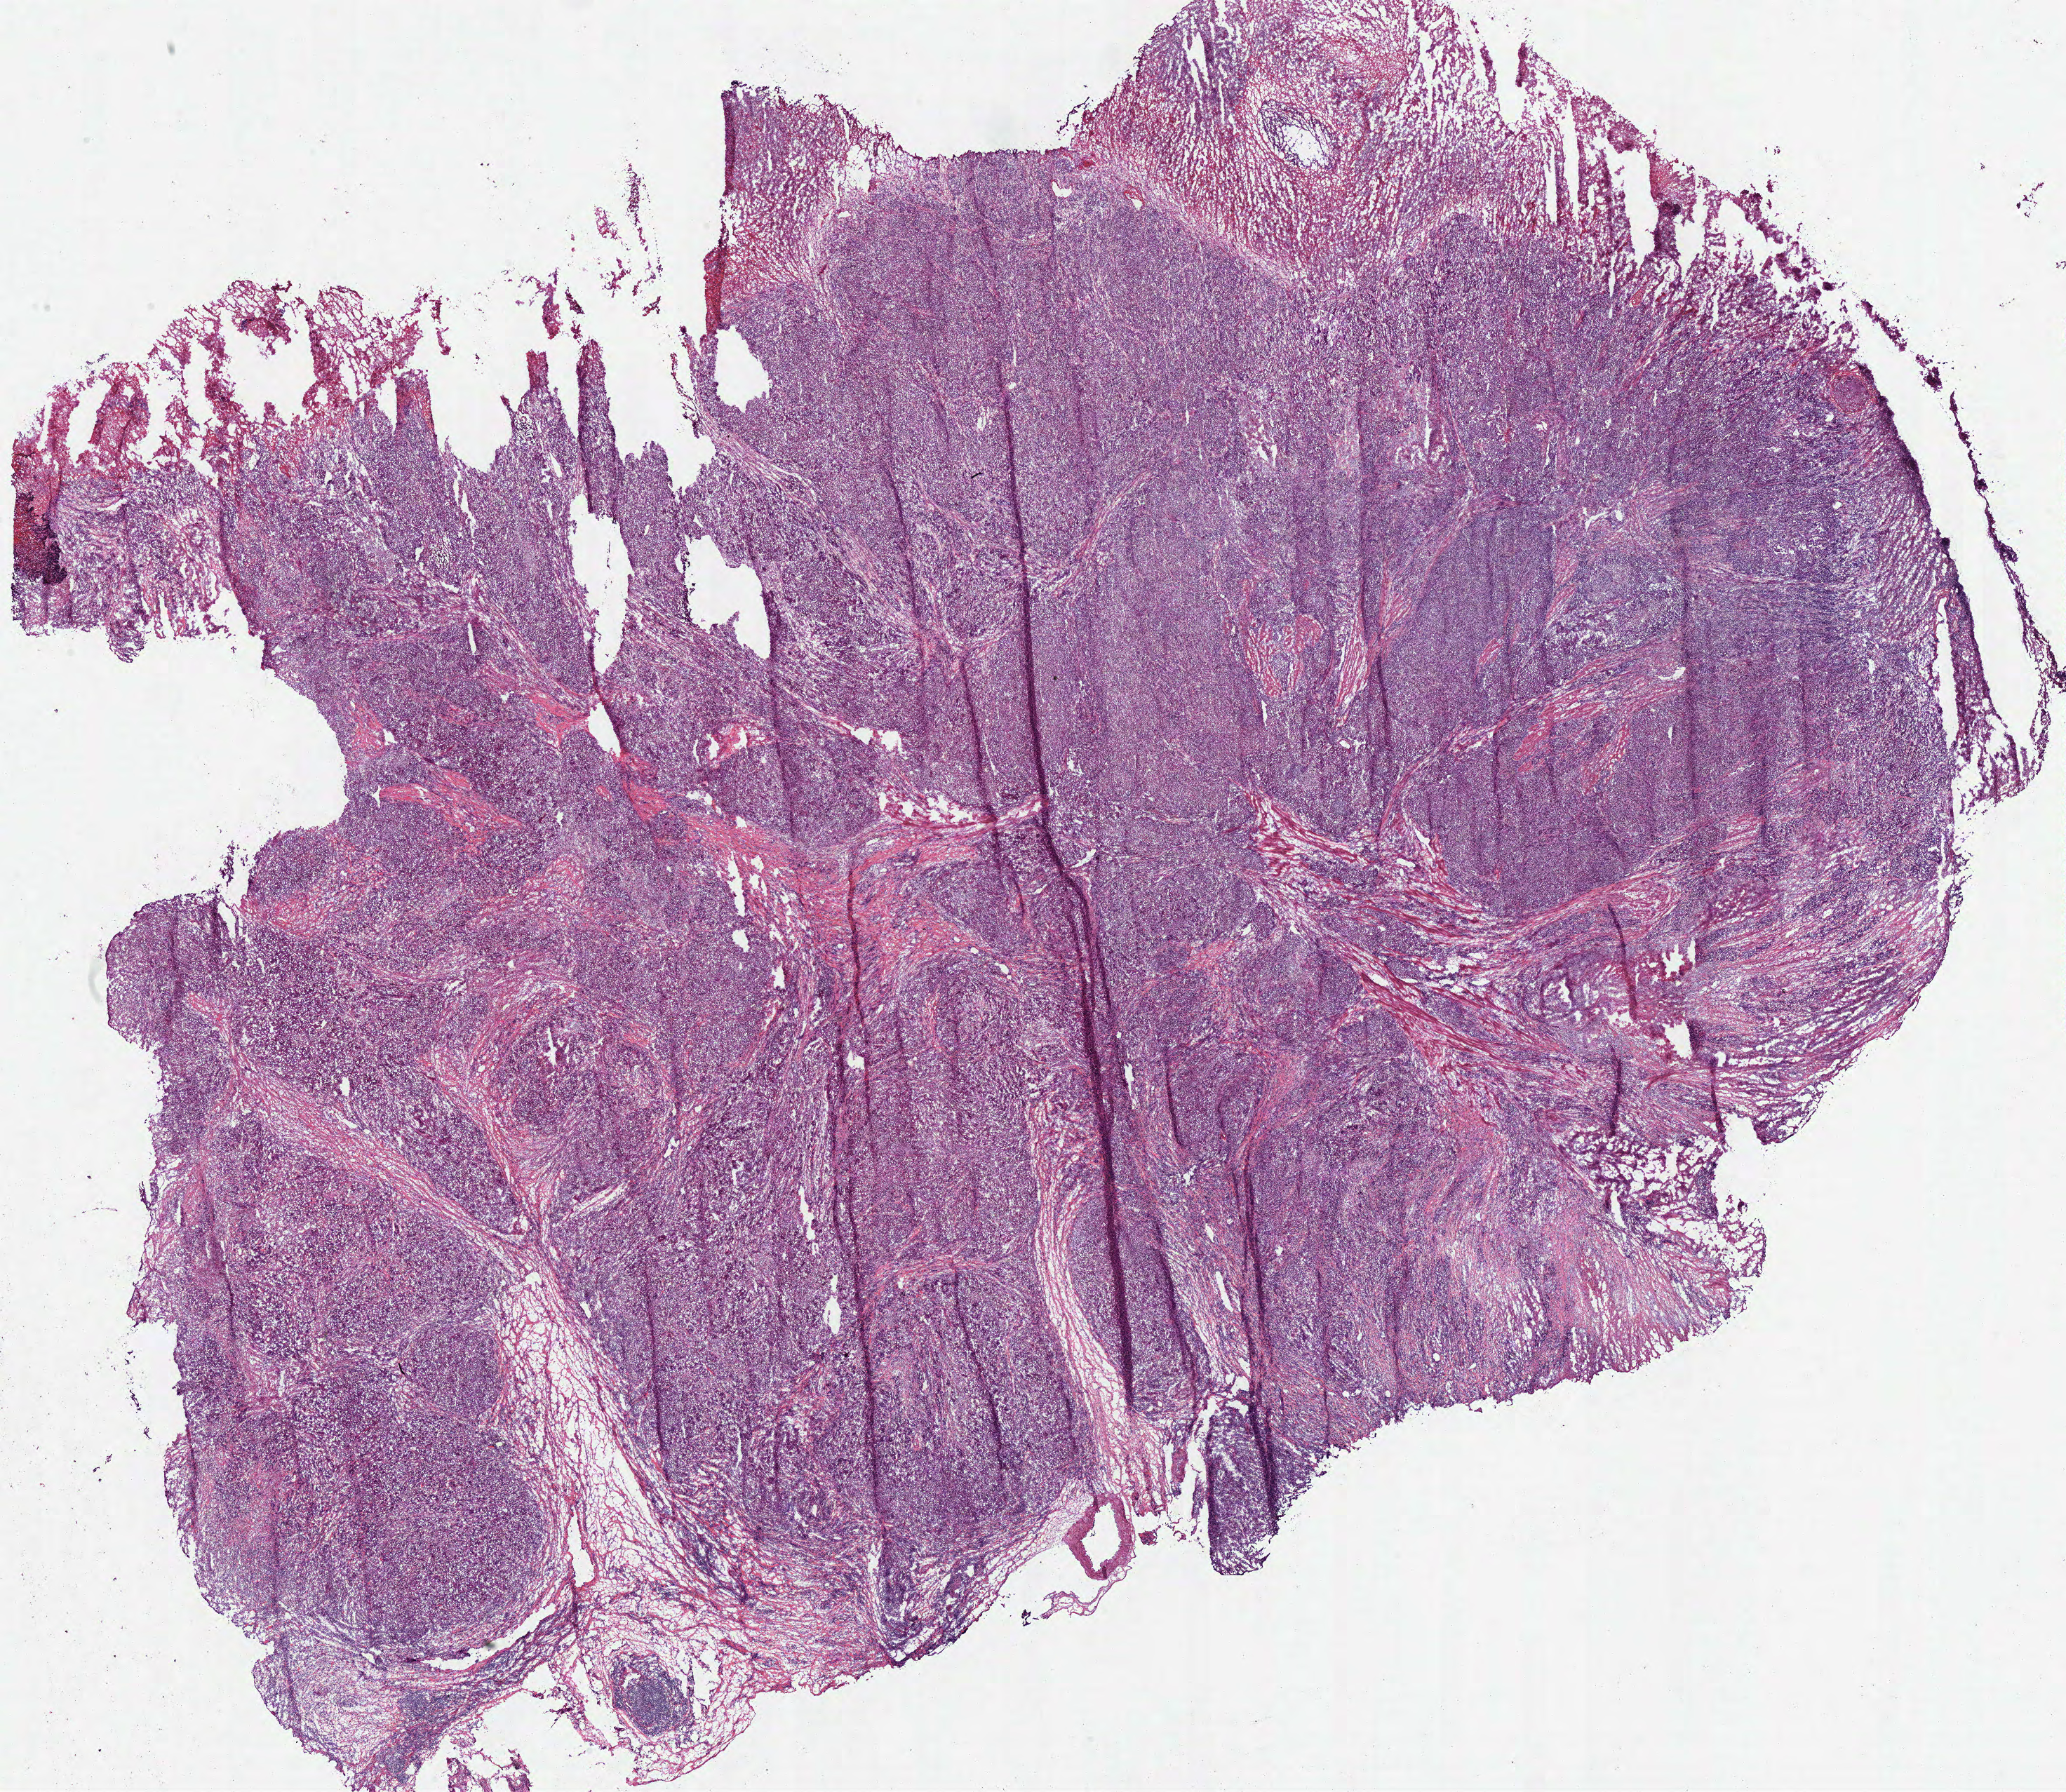
Digitized Hematoxylin and eosin (H&E) stained tissue section (whole slide) — whole scanned area (about 23.2 x 20.1 mm, acquisition: 40x scan) shown as a low-resolution overview, frozen section from the top of the tissue portion, sample: primary tumour, stomach. Female patient; age at initial diagnosis 64 years. Histologic grade: G3 (poorly differentiated). Slide review estimates, as recorded: tumour cells 95%, tumour nuclei 90%, normal cells 0%, stromal cells 5%, necrosis 0%.
Pathologic diagnosis: Adenocarcinoma, NOS (cardia, NOS). Lymph nodes positive (case pathology): 0 of 15 examined. AJCC pathologic stage: IIA (7th edition).